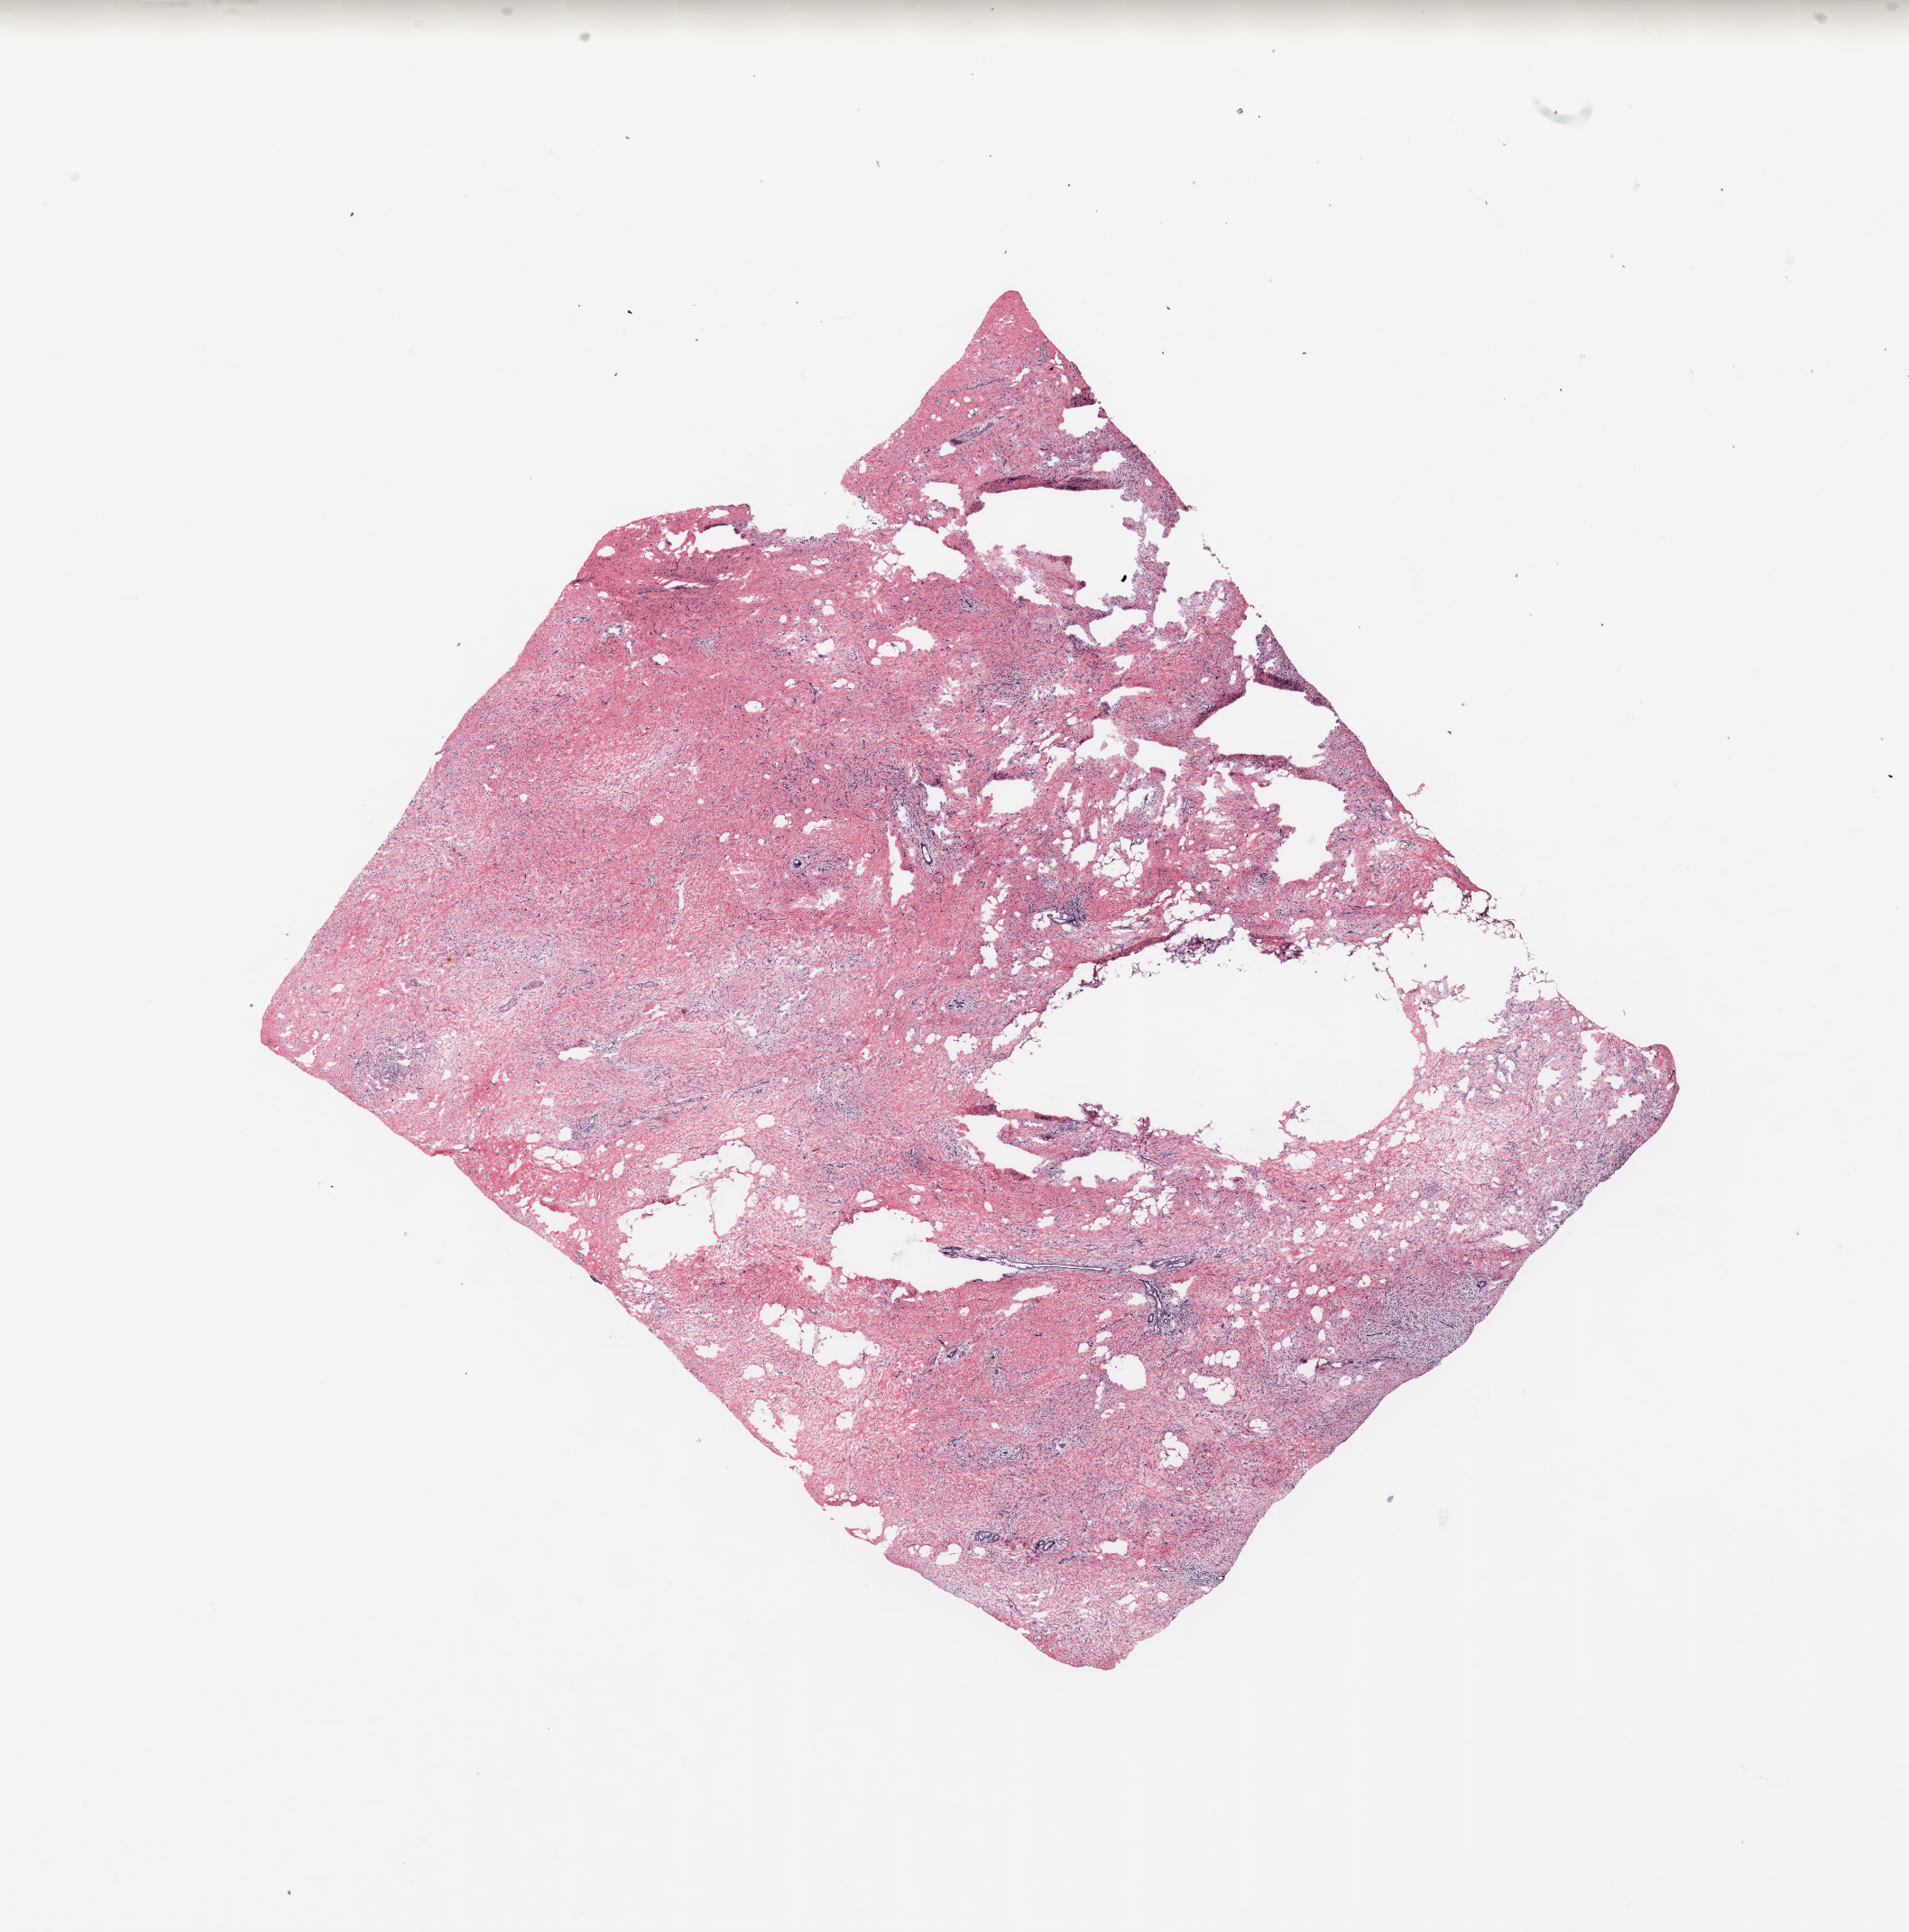
Digitized H&E tissue section (whole slide), low-resolution overview of the scanned area, about 16.7 x 16.9 mm, breast, tissue type not recorded.
* patient diagnosis (cohort enrolment): breast cancer (breast)